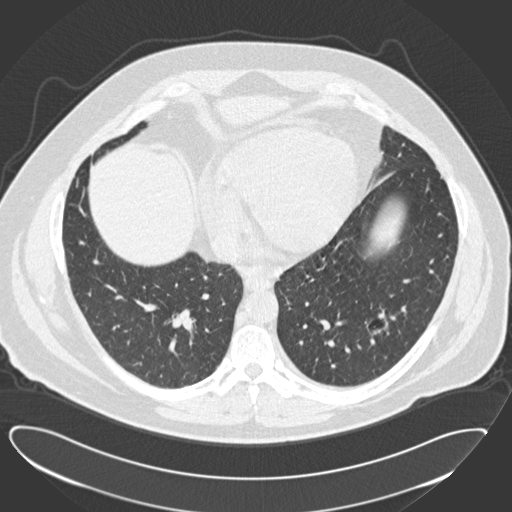
Chest CT (low-dose screening protocol), one axial image, first (baseline) screen, lung window (W 1500 / L -600 HU), 2 mm slice thickness, standard (soft-tissue) reconstruction kernel (B30f). Male participant, aged 57 years at enrolment. Current smoker at enrolment.
Expert reader's lesion annotation, bounding box [x1, y1, x2, y2] px = [357, 303, 411, 357]. The screening reader recorded 2 non-calcified nodules or masses ≥4 mm on this exam; which of them this box marks is not recorded. Lung cancer was diagnosed 791 days after this screen: squamous cell carcinoma, NOS, left lower lobe, moderately differentiated (G2), stage IA (AJCC 6th edition), 22 mm at pathology.